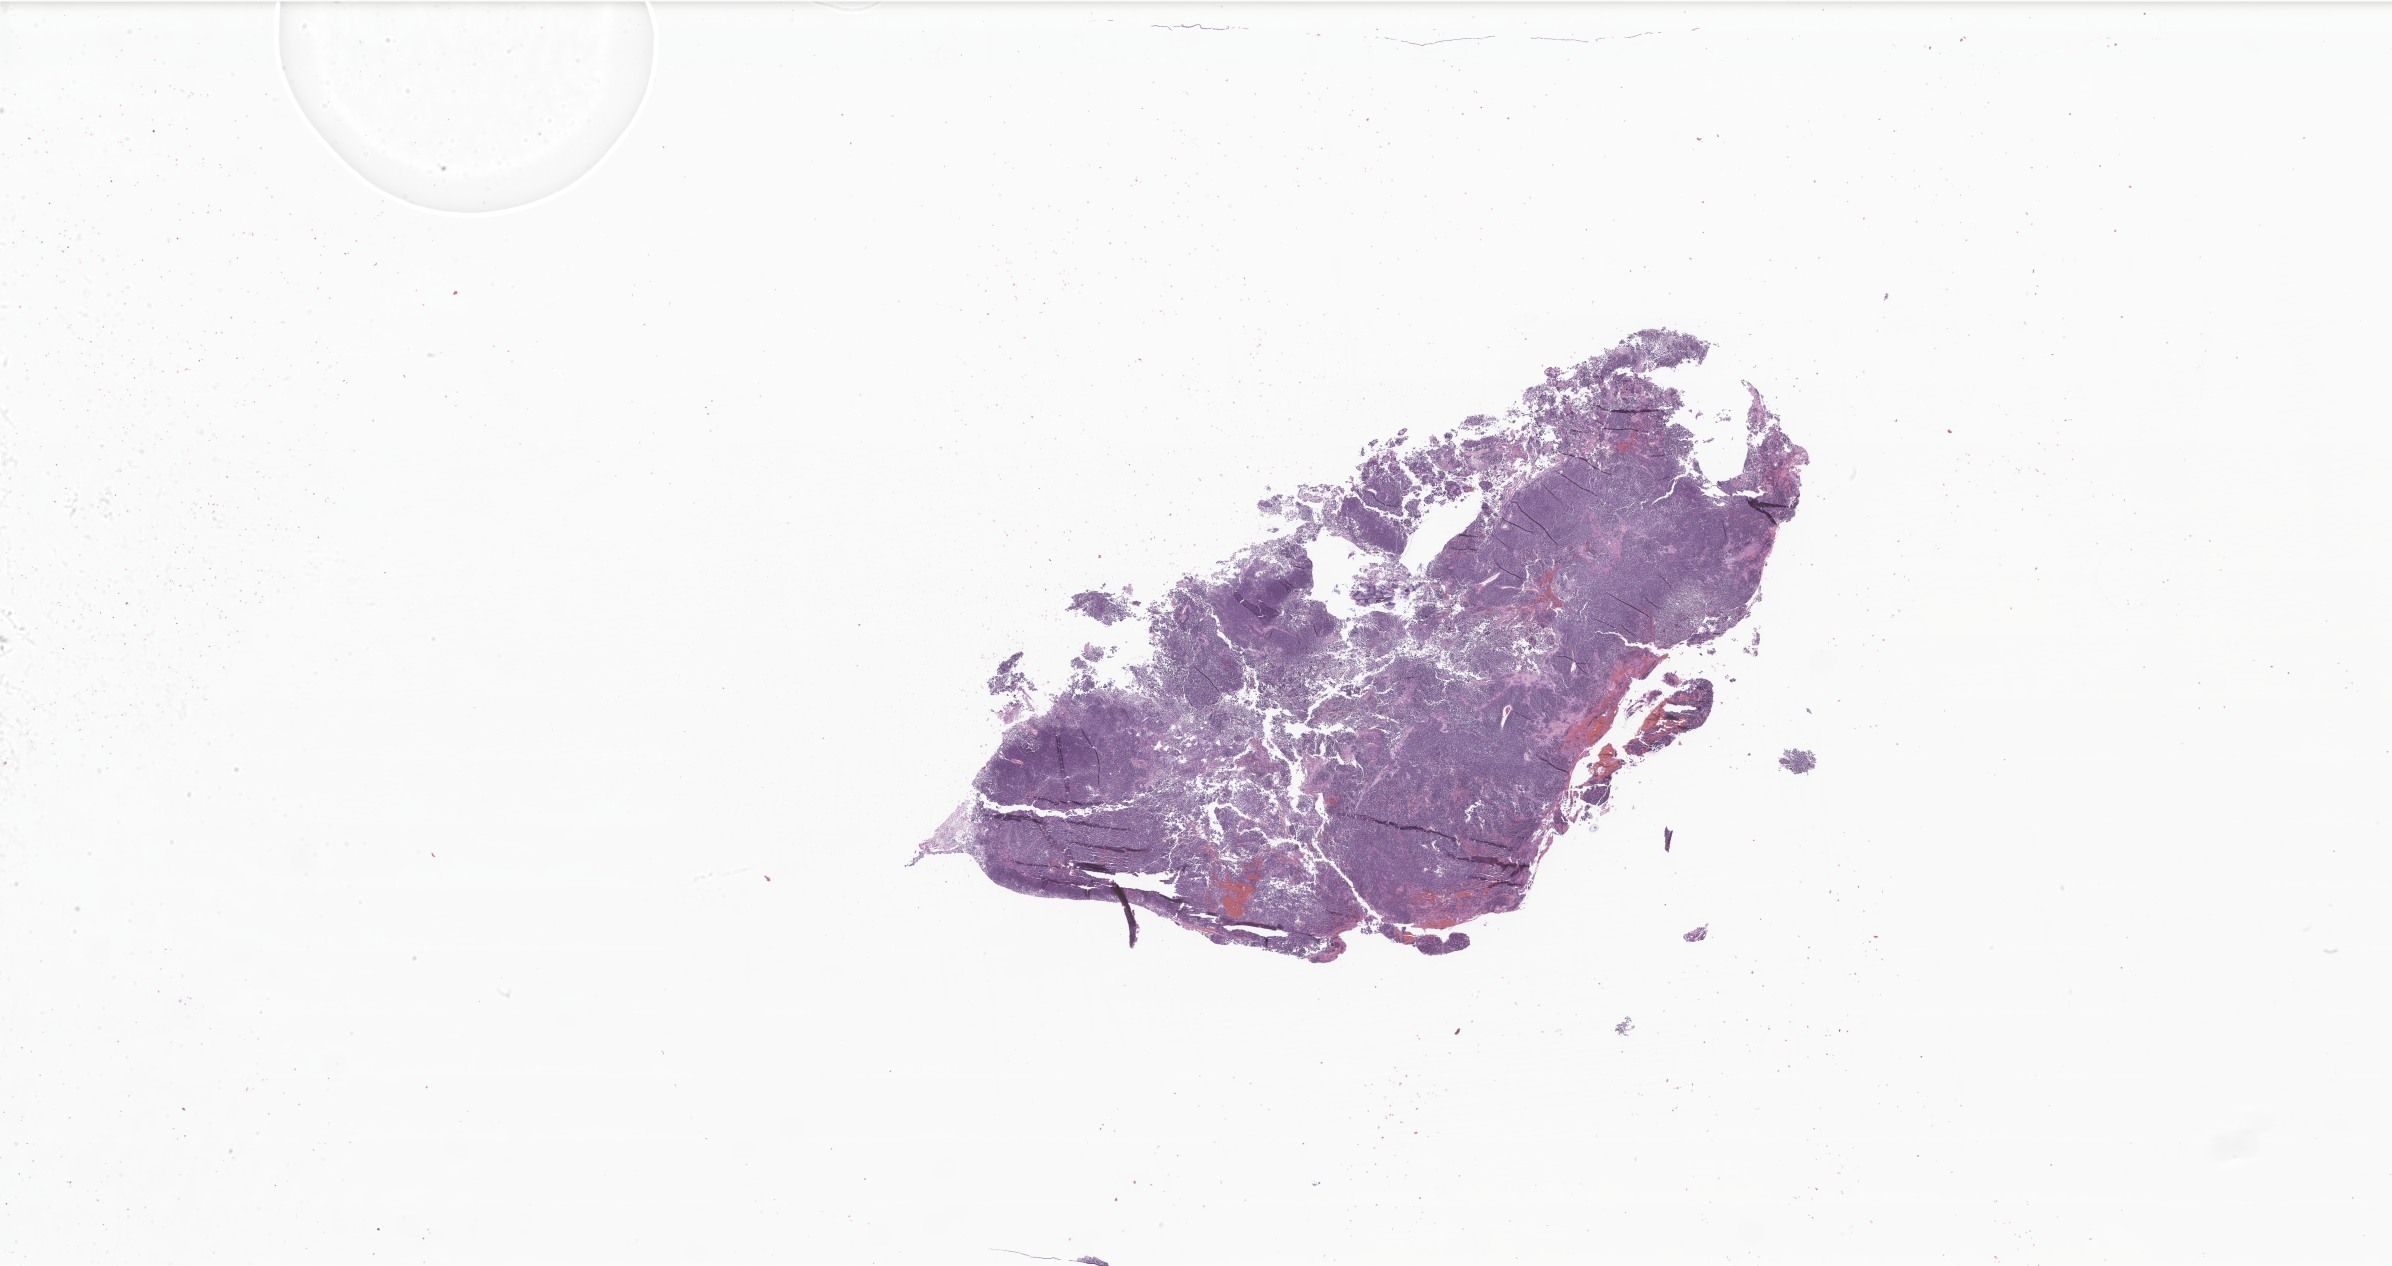
Digitized H&E-stained section of tumor tissue from the brain, a low-resolution overview of the entire scanned area, about 40.3 x 21.4 mm, formalin-fixed, paraffin-embedded (FFPE) tissue. Male patient, age 39 months (3 years 3 months).
Diagnosis (ICD-O-3 morphology term): Neoplasm, malignant.